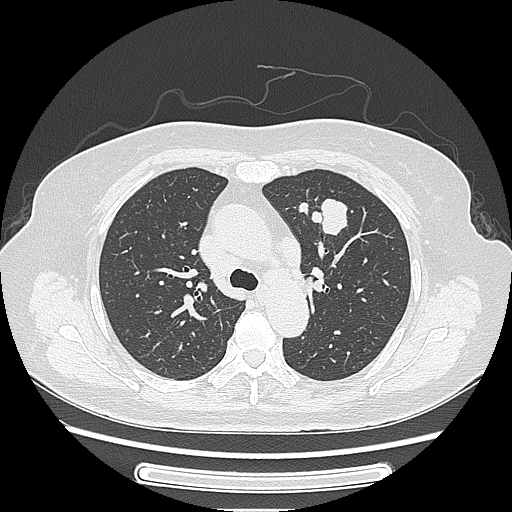
Chest CT, one axial slice; reconstruction kernel LUNG; lung window (W 1500 / L -600 HU); 1.25 mm slice thickness; 512 × 512 image matrix, field of view 363 × 363 mm. Female patient, age 77 years. Case-level facts recorded for this patient, not image findings: clinical TNM (as recorded): T1c N3 M0; histopathological grade: G2-3.
Structures marked on this image (bounding box drawn by a radiologist):
- lung tumour (recorded histology: adenocarcinoma): bounding box <312,192,360,240> (left, top, right, bottom; pixels)